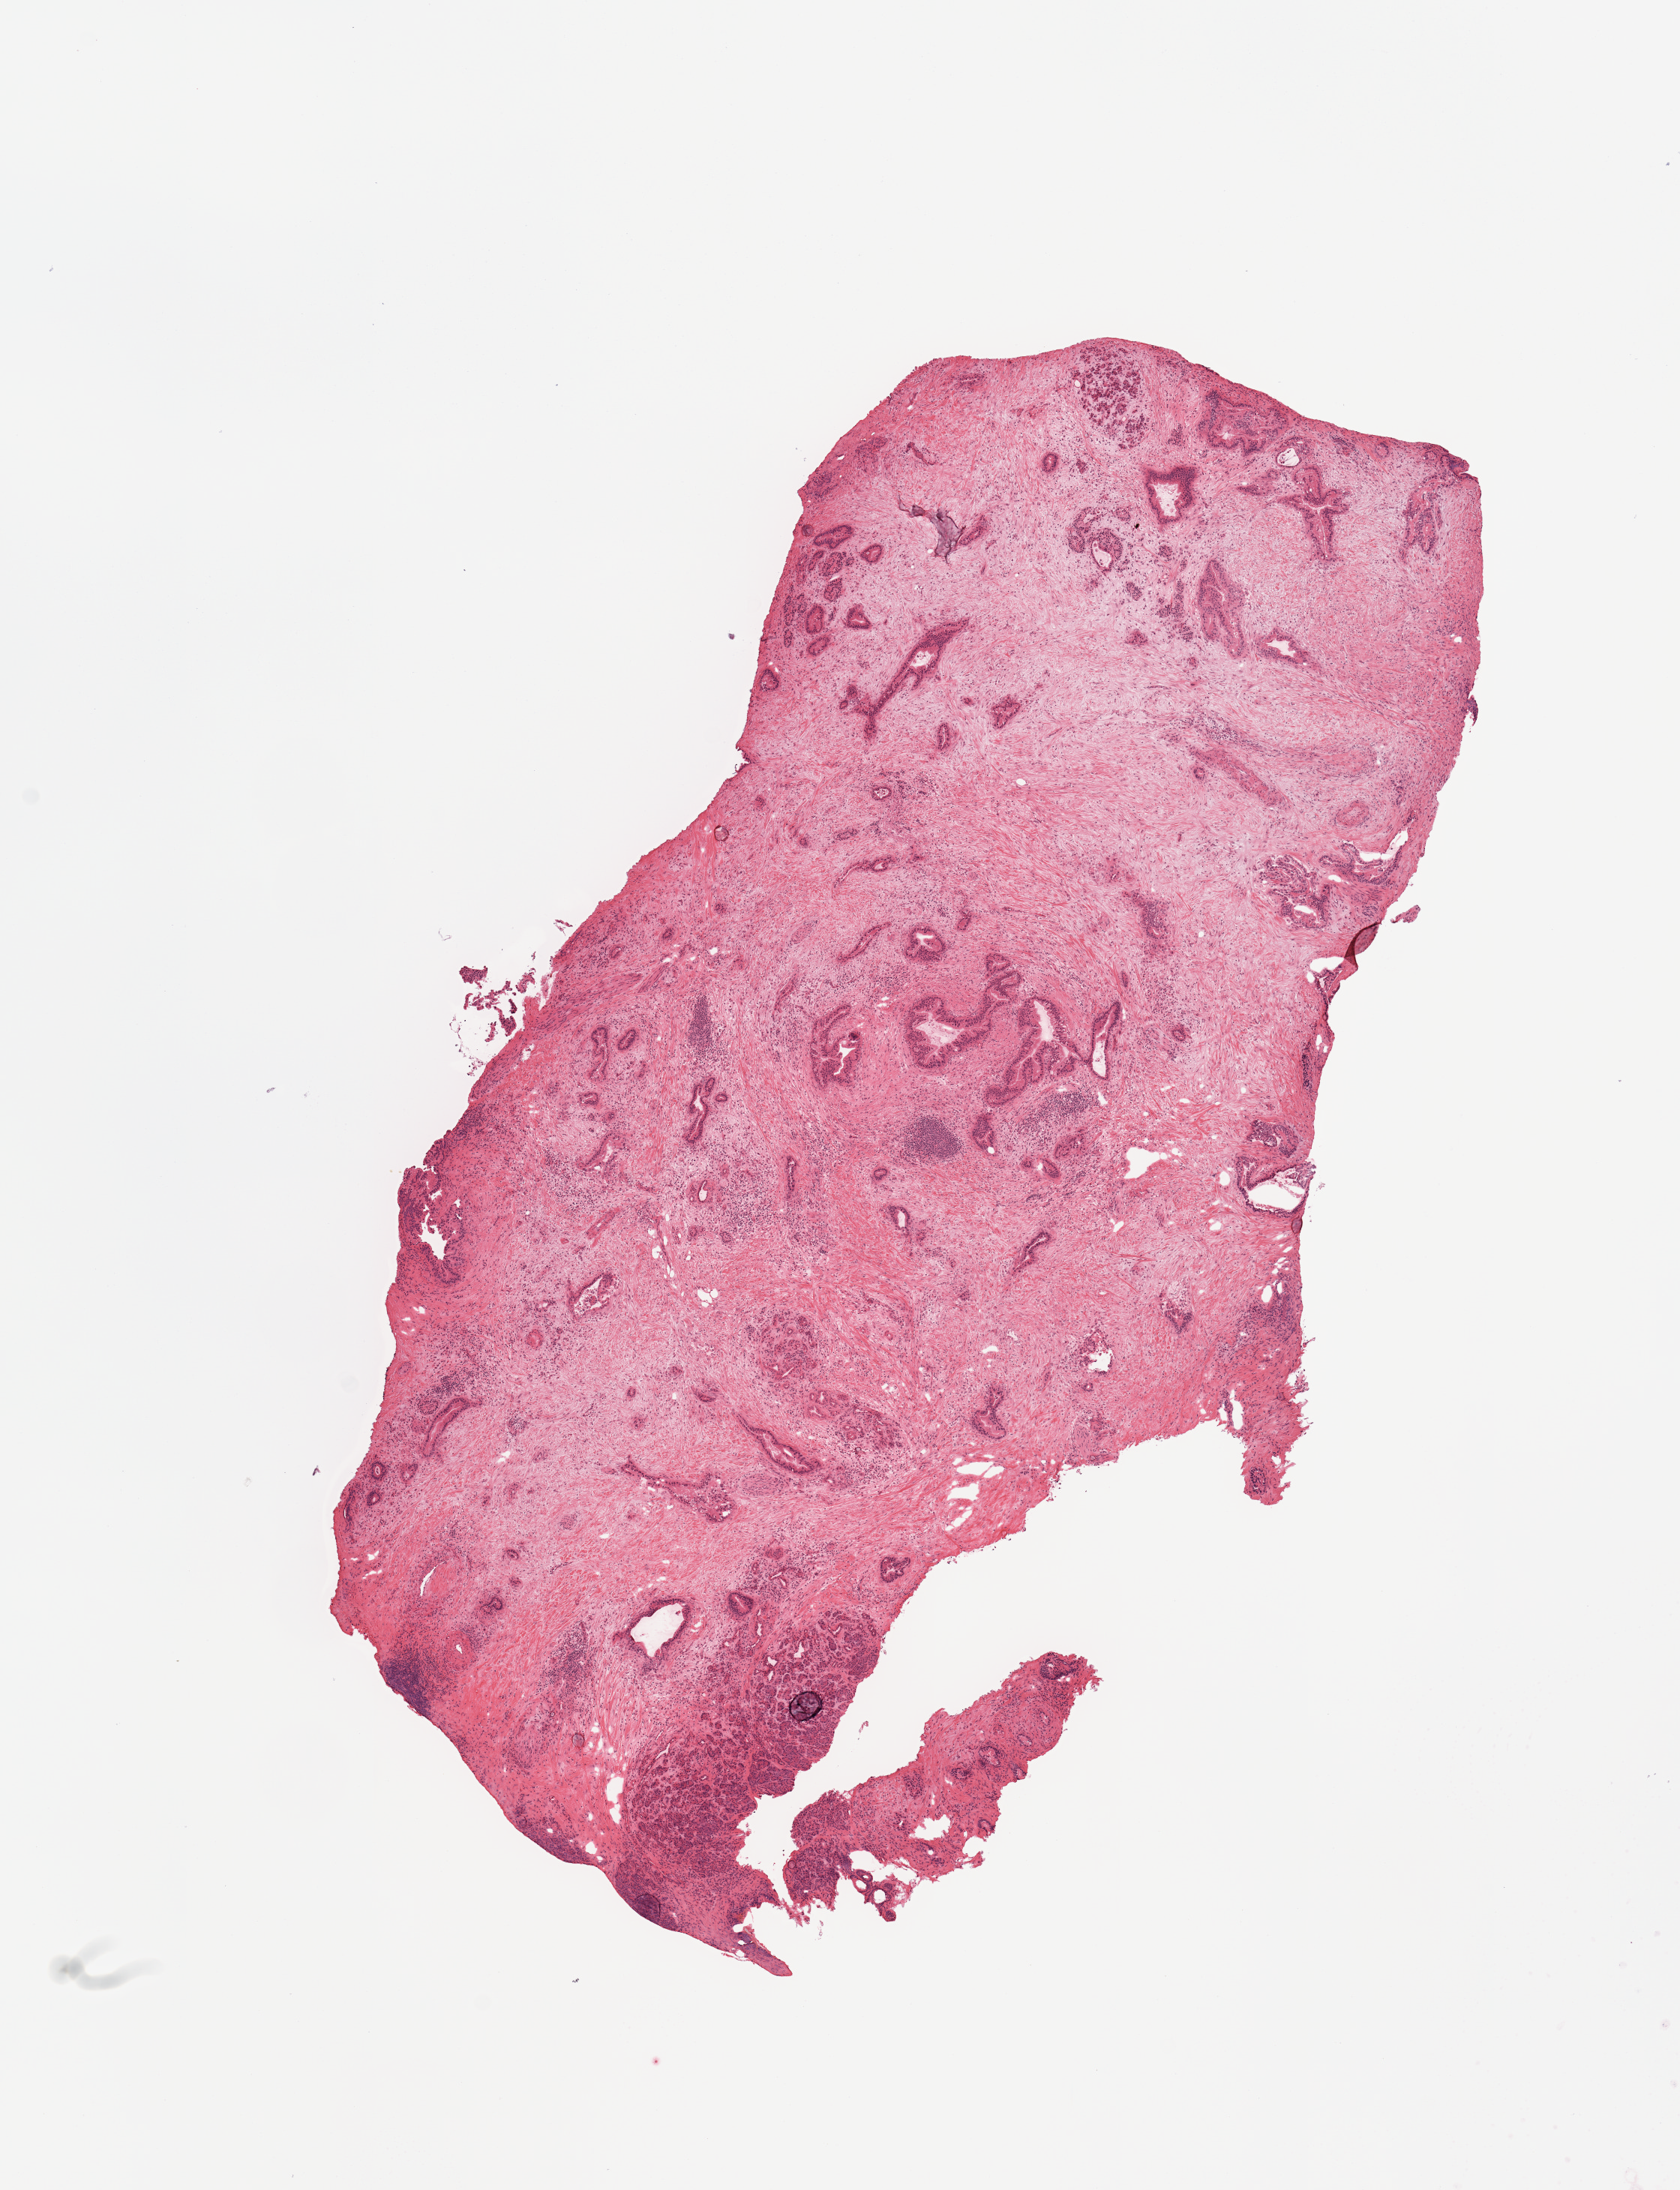
H&E-stained whole-slide image, low-resolution overview of the scanned area, about 8.9 x 11.5 mm (slide scanned at 20x), tumour tissue sample, sampled site: pancreas. 62-year-old male patient. Histologic grade: G1 (well differentiated). Slide review estimates, as recorded: tumour nuclei 25%, necrosis 0%.
• AJCC pathologic stage: IIB
• diagnosis: Infiltrating duct carcinoma, NOS